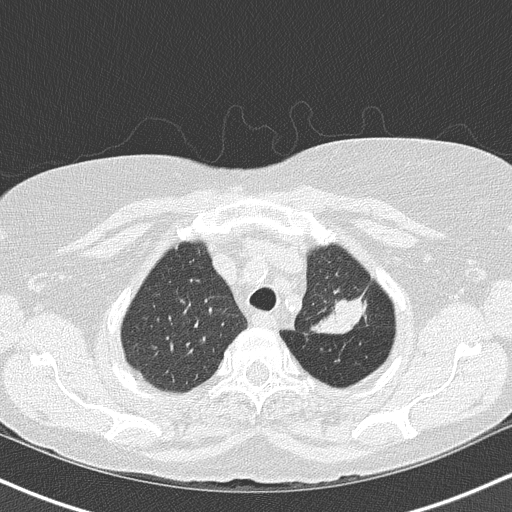
Low-dose screening chest CT, axial slice; third annual screen; lung window (W 1500 / L -600 HU); lung (sharp) reconstruction kernel (B50f); 120 kVp; 512 × 512 image matrix, field of view 320 × 320 mm. Female participant, aged 68 years at enrolment.
Expert reader's lesion annotation, box from (x=289, y=236) to (x=379, y=342) px. Reader record for this screening exam (exam-level; its link to the box is not recorded): non-calcified nodule or mass ≥4 mm, left upper lobe, 5 × 5 mm, poorly defined margins, mixed attenuation, pre-existing on the prior screen: yes; interval growth: yes. Lung cancer was diagnosed 42 days after this screen: adenocarcinoma, NOS, left upper lobe, poorly differentiated (G3), stage IB (AJCC 6th edition), 50 mm at pathology.